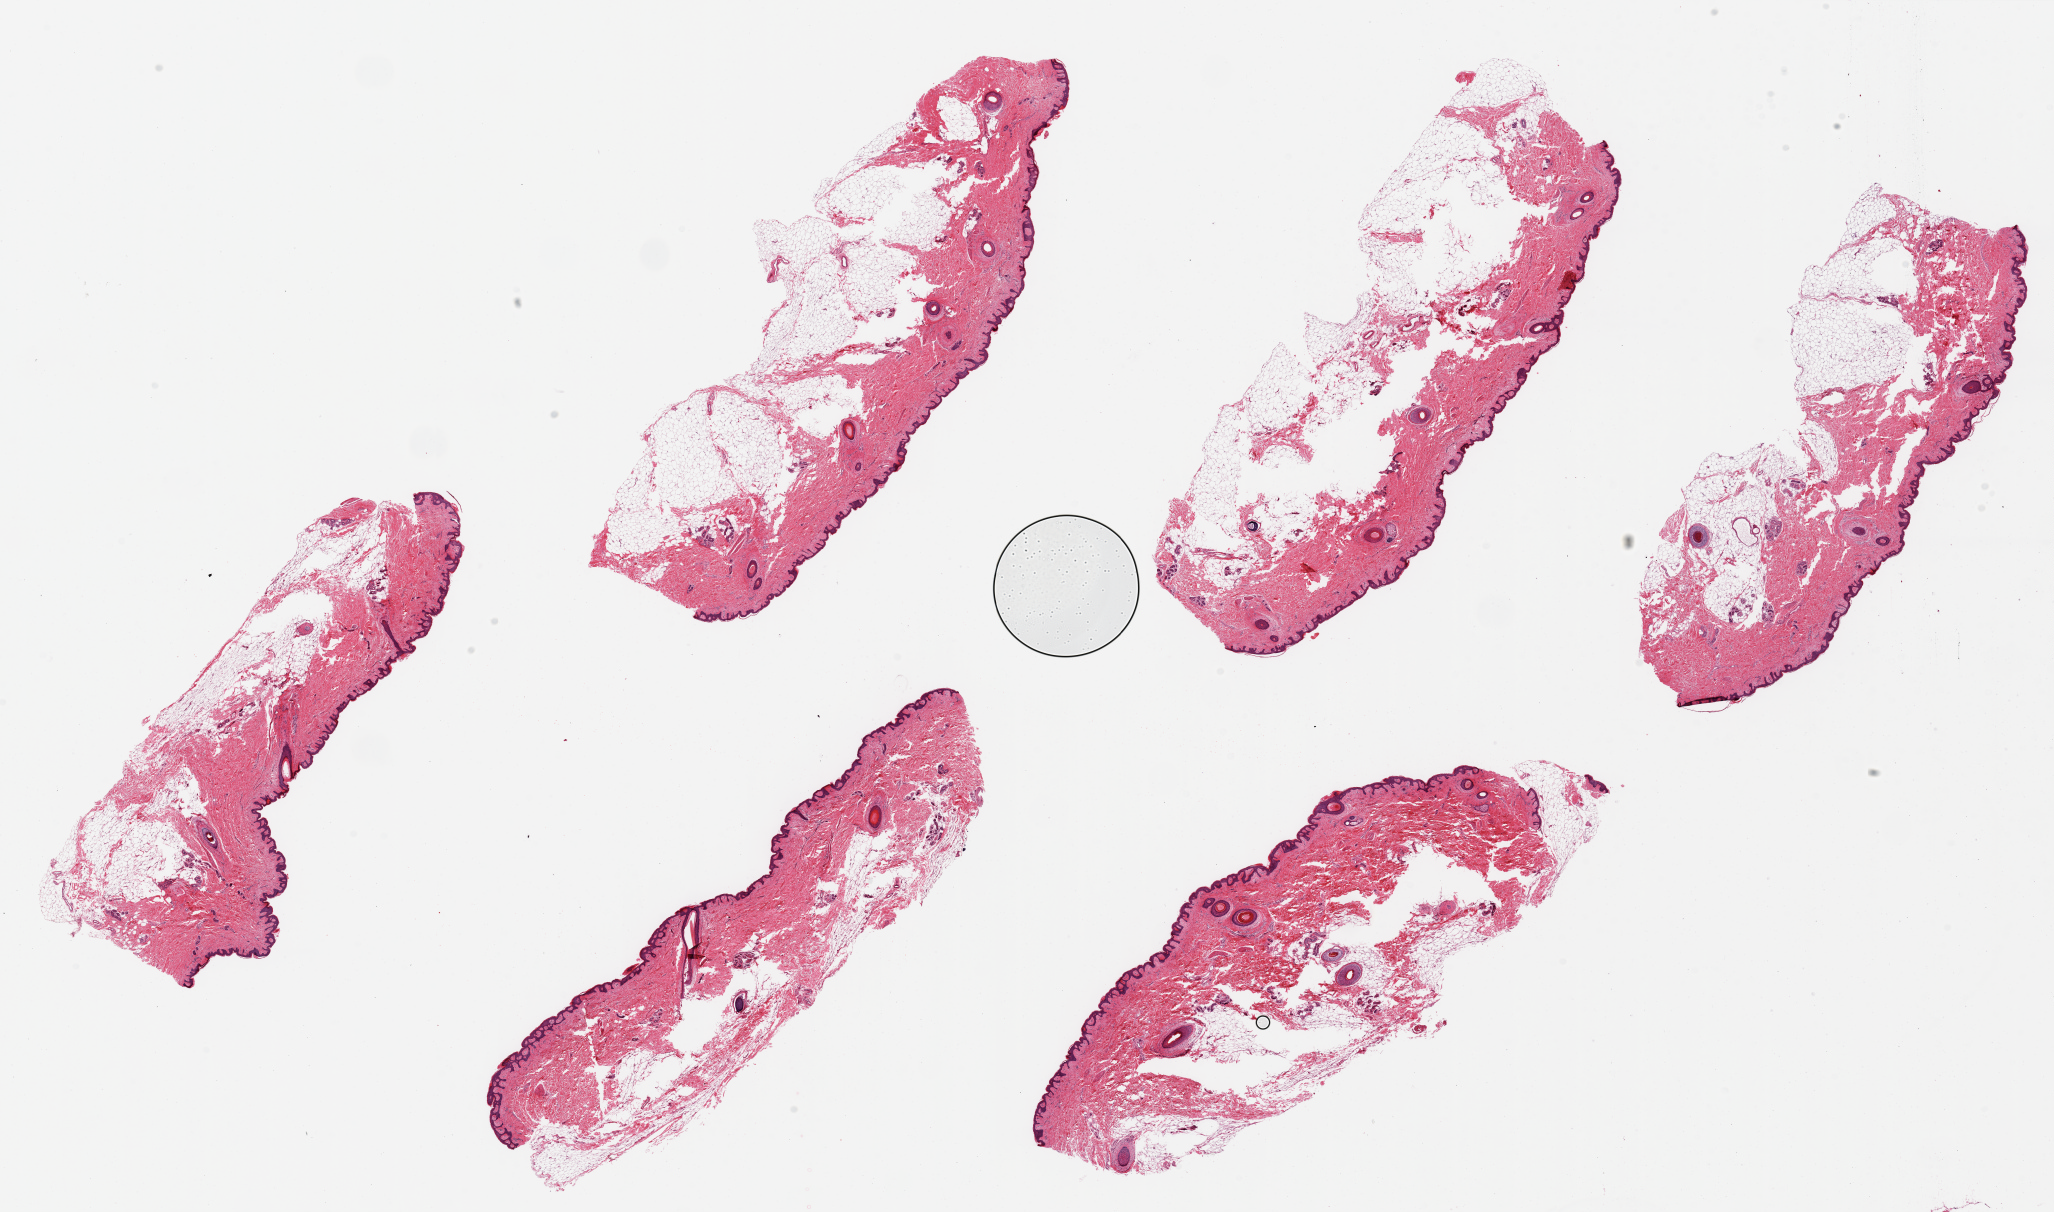
Haematoxylin and eosin whole-slide image, brightfield, low-resolution overview of the scanned area, about 32.5 x 19.2 mm (slide scanned at 20x), PAXgene-fixed paraffin-embedded (PFPE) section, target tissue: skin of suprapubic region, tissue donor sample. Donor: female.
Reviewer comment on this tissue sample: 6 pieces ~10x3mm. Squamous epithelium looks atrophic, <1% thickness.